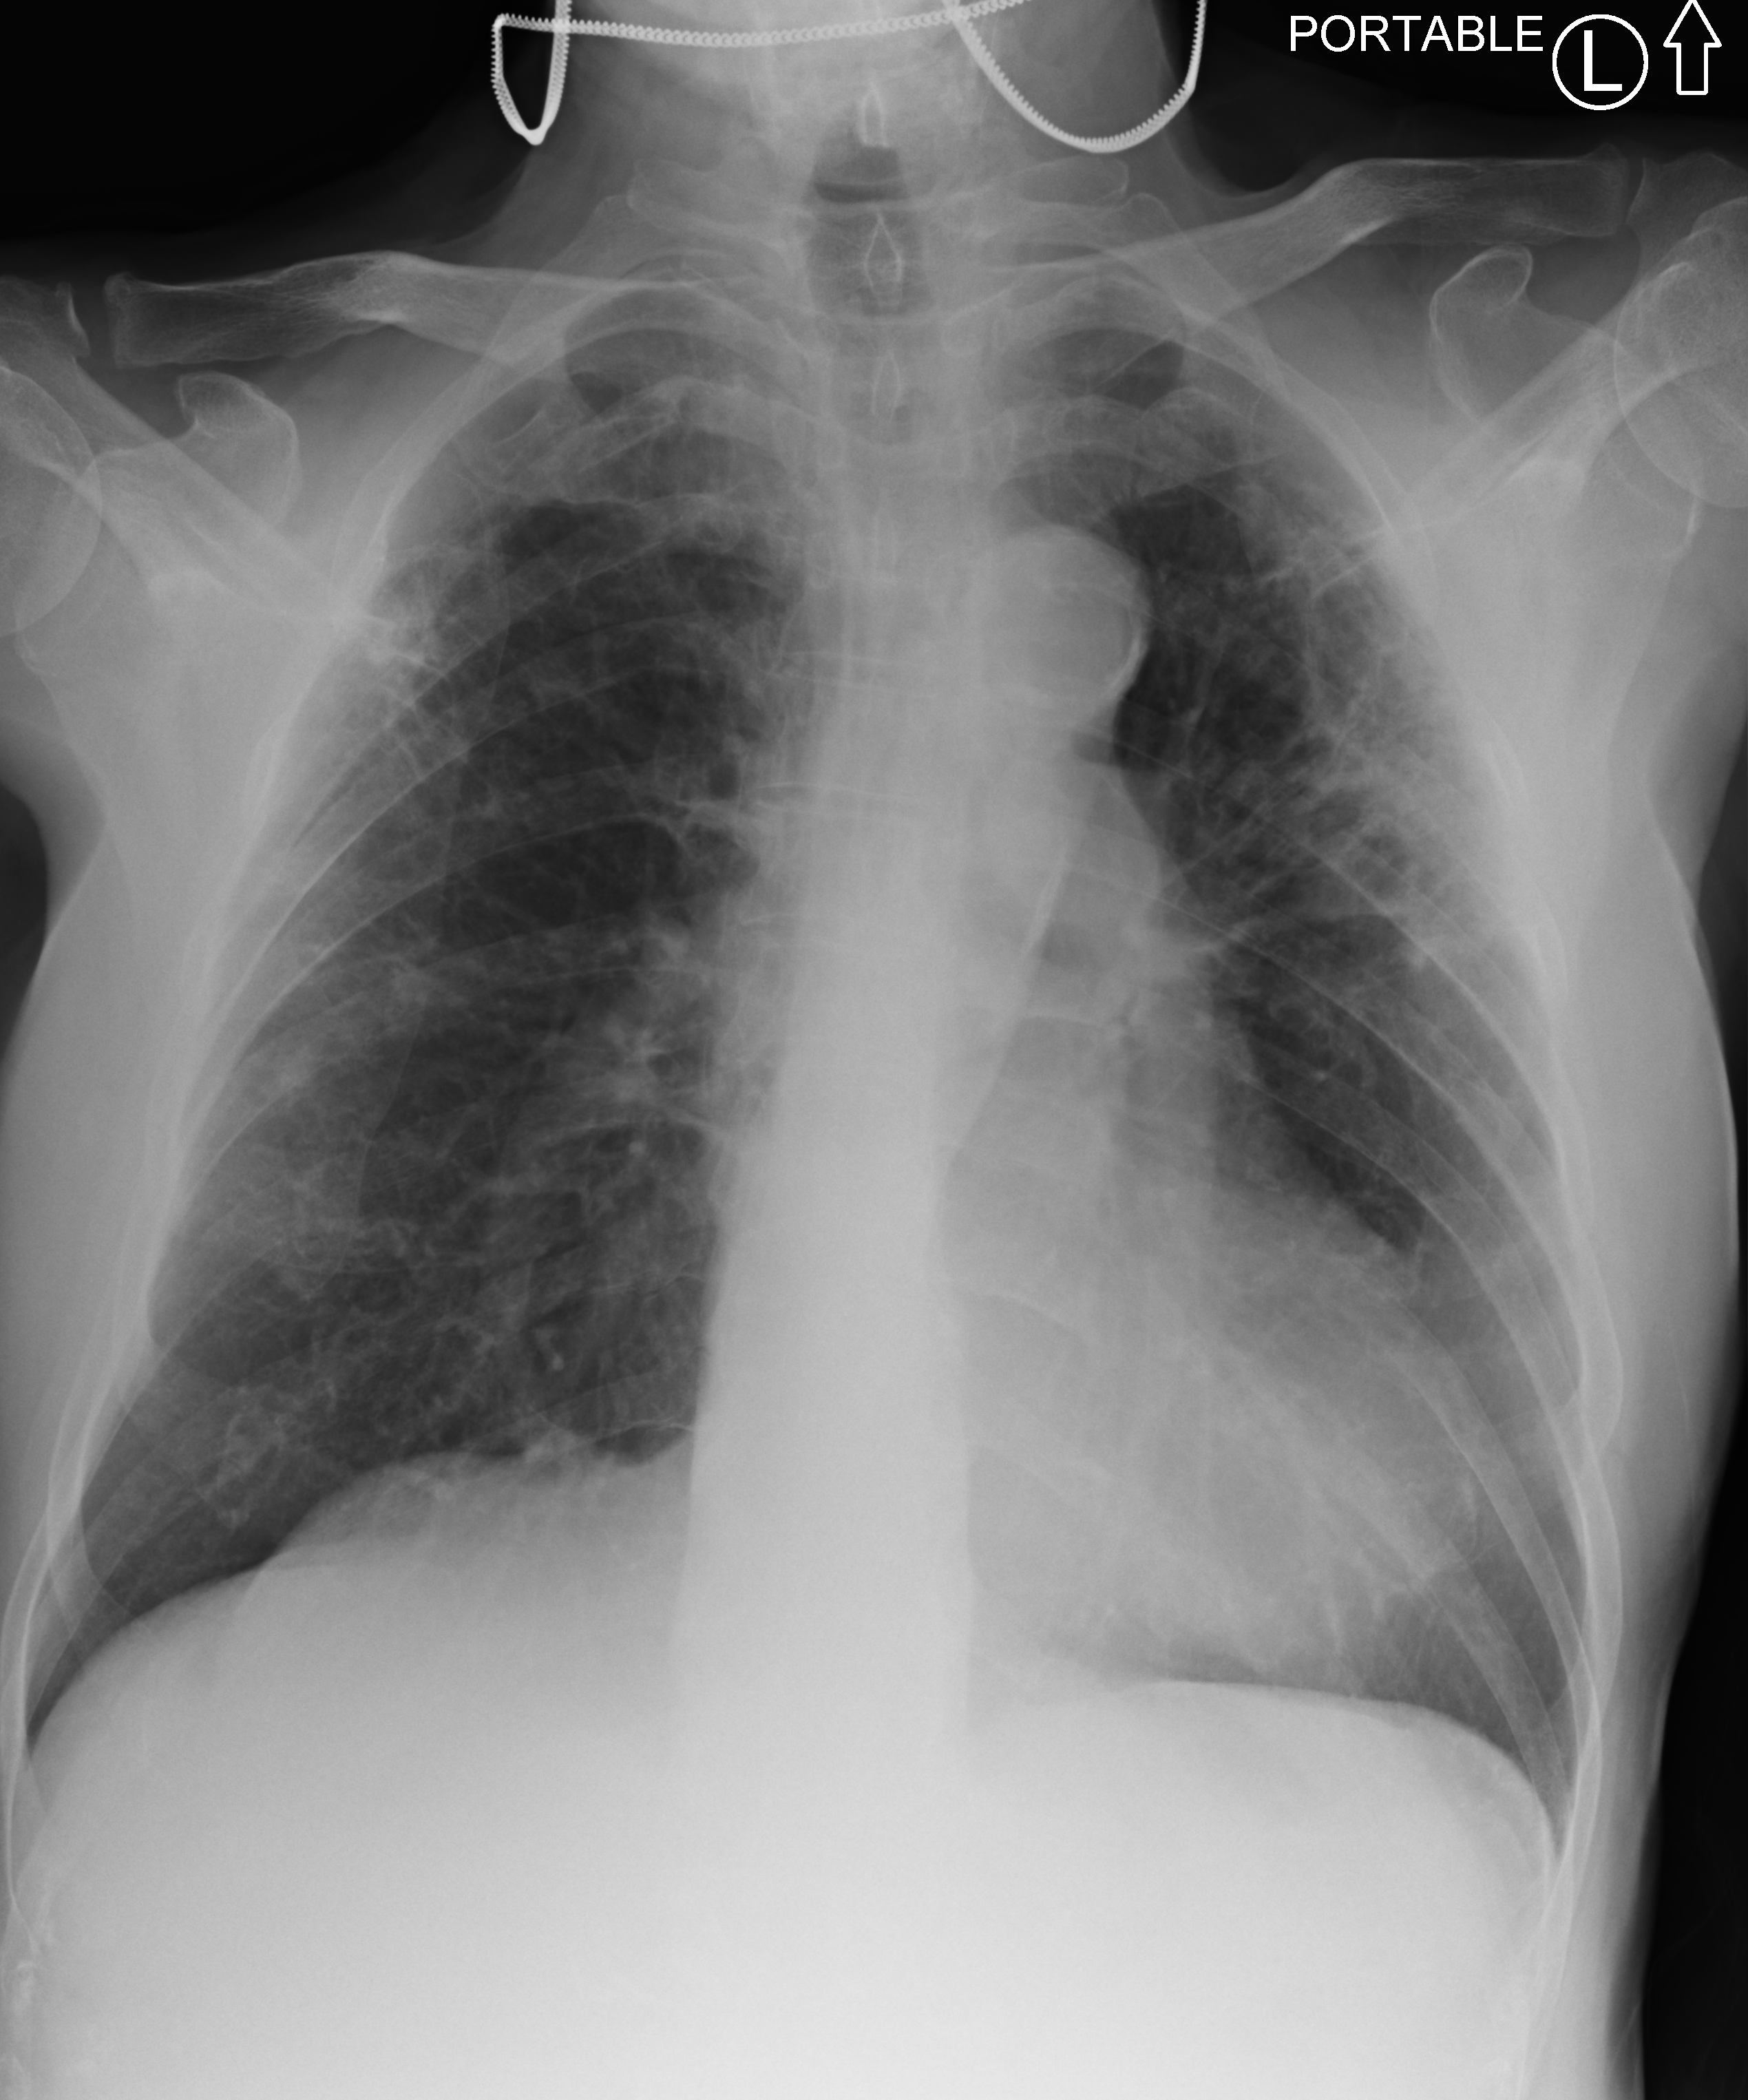
Bedside chest radiograph (computed radiography); anteroposterior (AP) projection. Male patient hospitalised with COVID-19, age 75–90 years.
Admission-level facts for this patient (not findings on this image; timing relative to this image not recorded): mechanically ventilated during this hospital stay: no; length of hospital stay: 3 days; admitted to intensive care during this hospital stay: no.